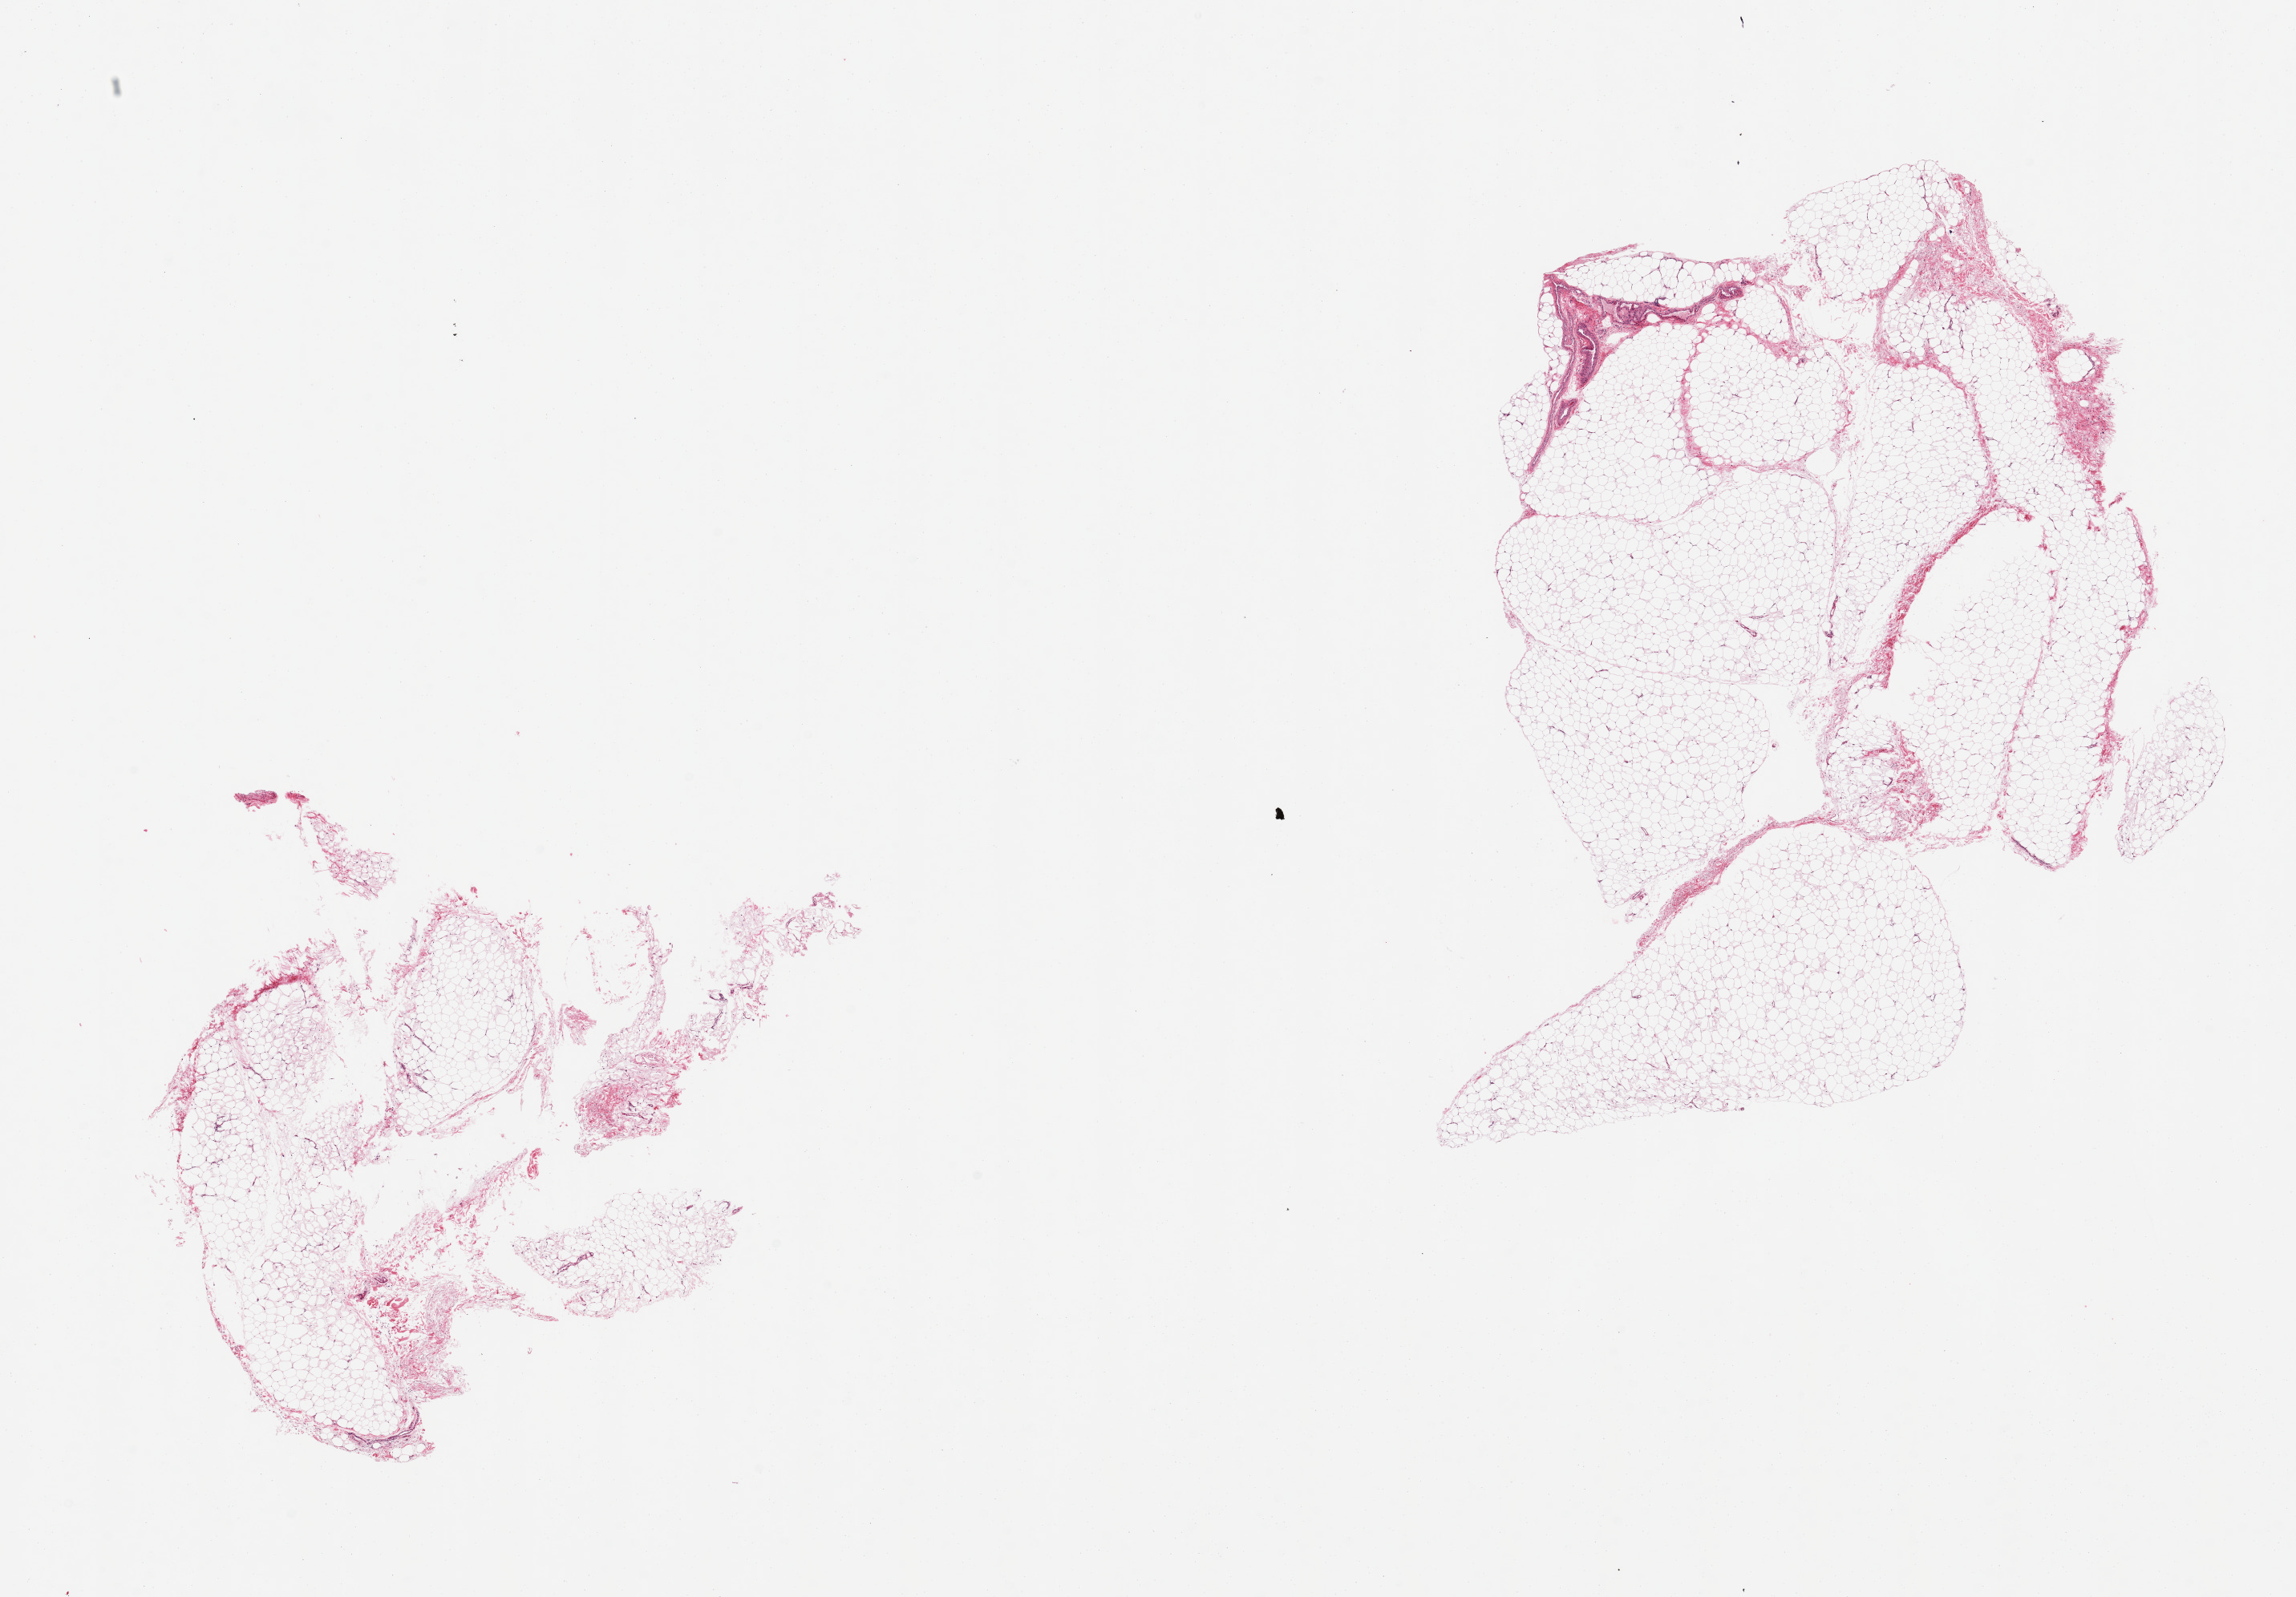
Digitized haematoxylin and eosin-stained section, brightfield — low-resolution overview of the scanned area, about 22.6 x 15.8 mm, PAXgene-fixed paraffin-embedded (PFPE) section, section of adipose tissue (target tissue), tissue donor sample. Donor sex: male.
Pathologist's review note for this sample: 2 pieces, ~10% fascia/vascular elements.